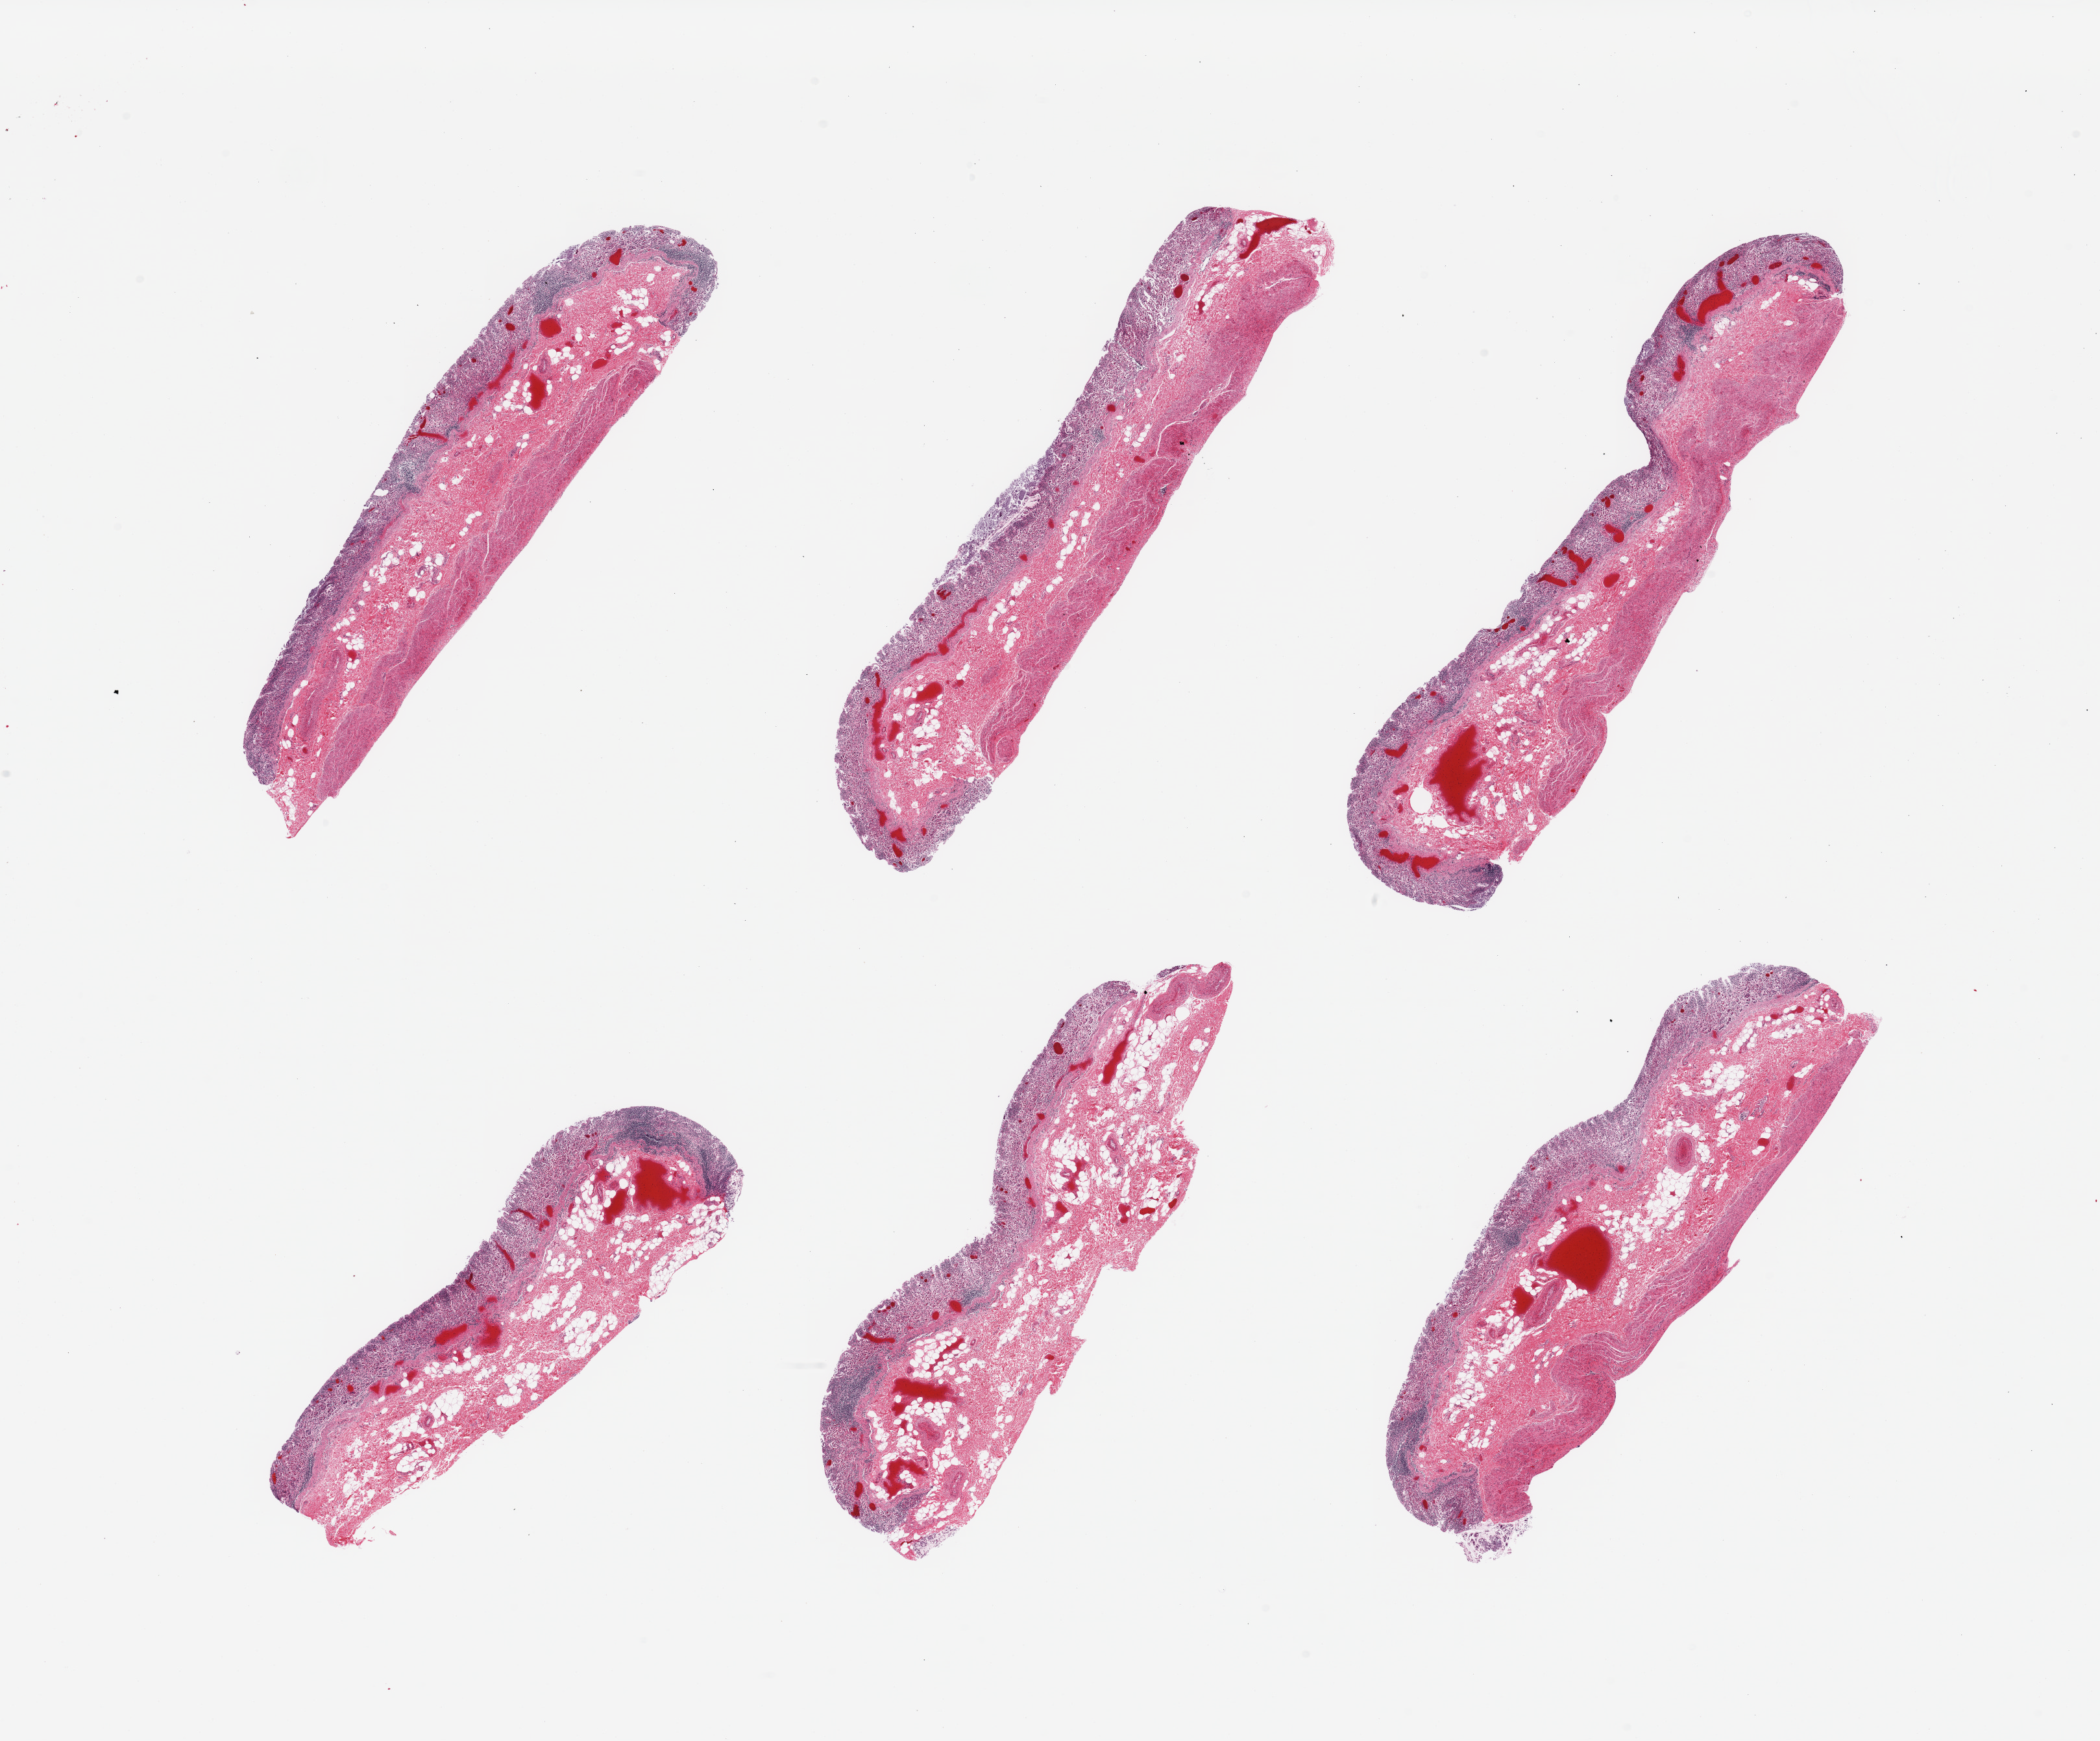
H&E whole-slide image, low-resolution overview of the scanned area, about 25.6 x 21.2 mm (acquisition: 20x scan); PAXgene-fixed paraffin-embedded (PFPE) section; sampled site (target tissue): stomach; tissue donor sample. Donor sex: male.
Review note (as recorded): 6 pieces; mucosa totally autolyzed; 2 without muscularis.